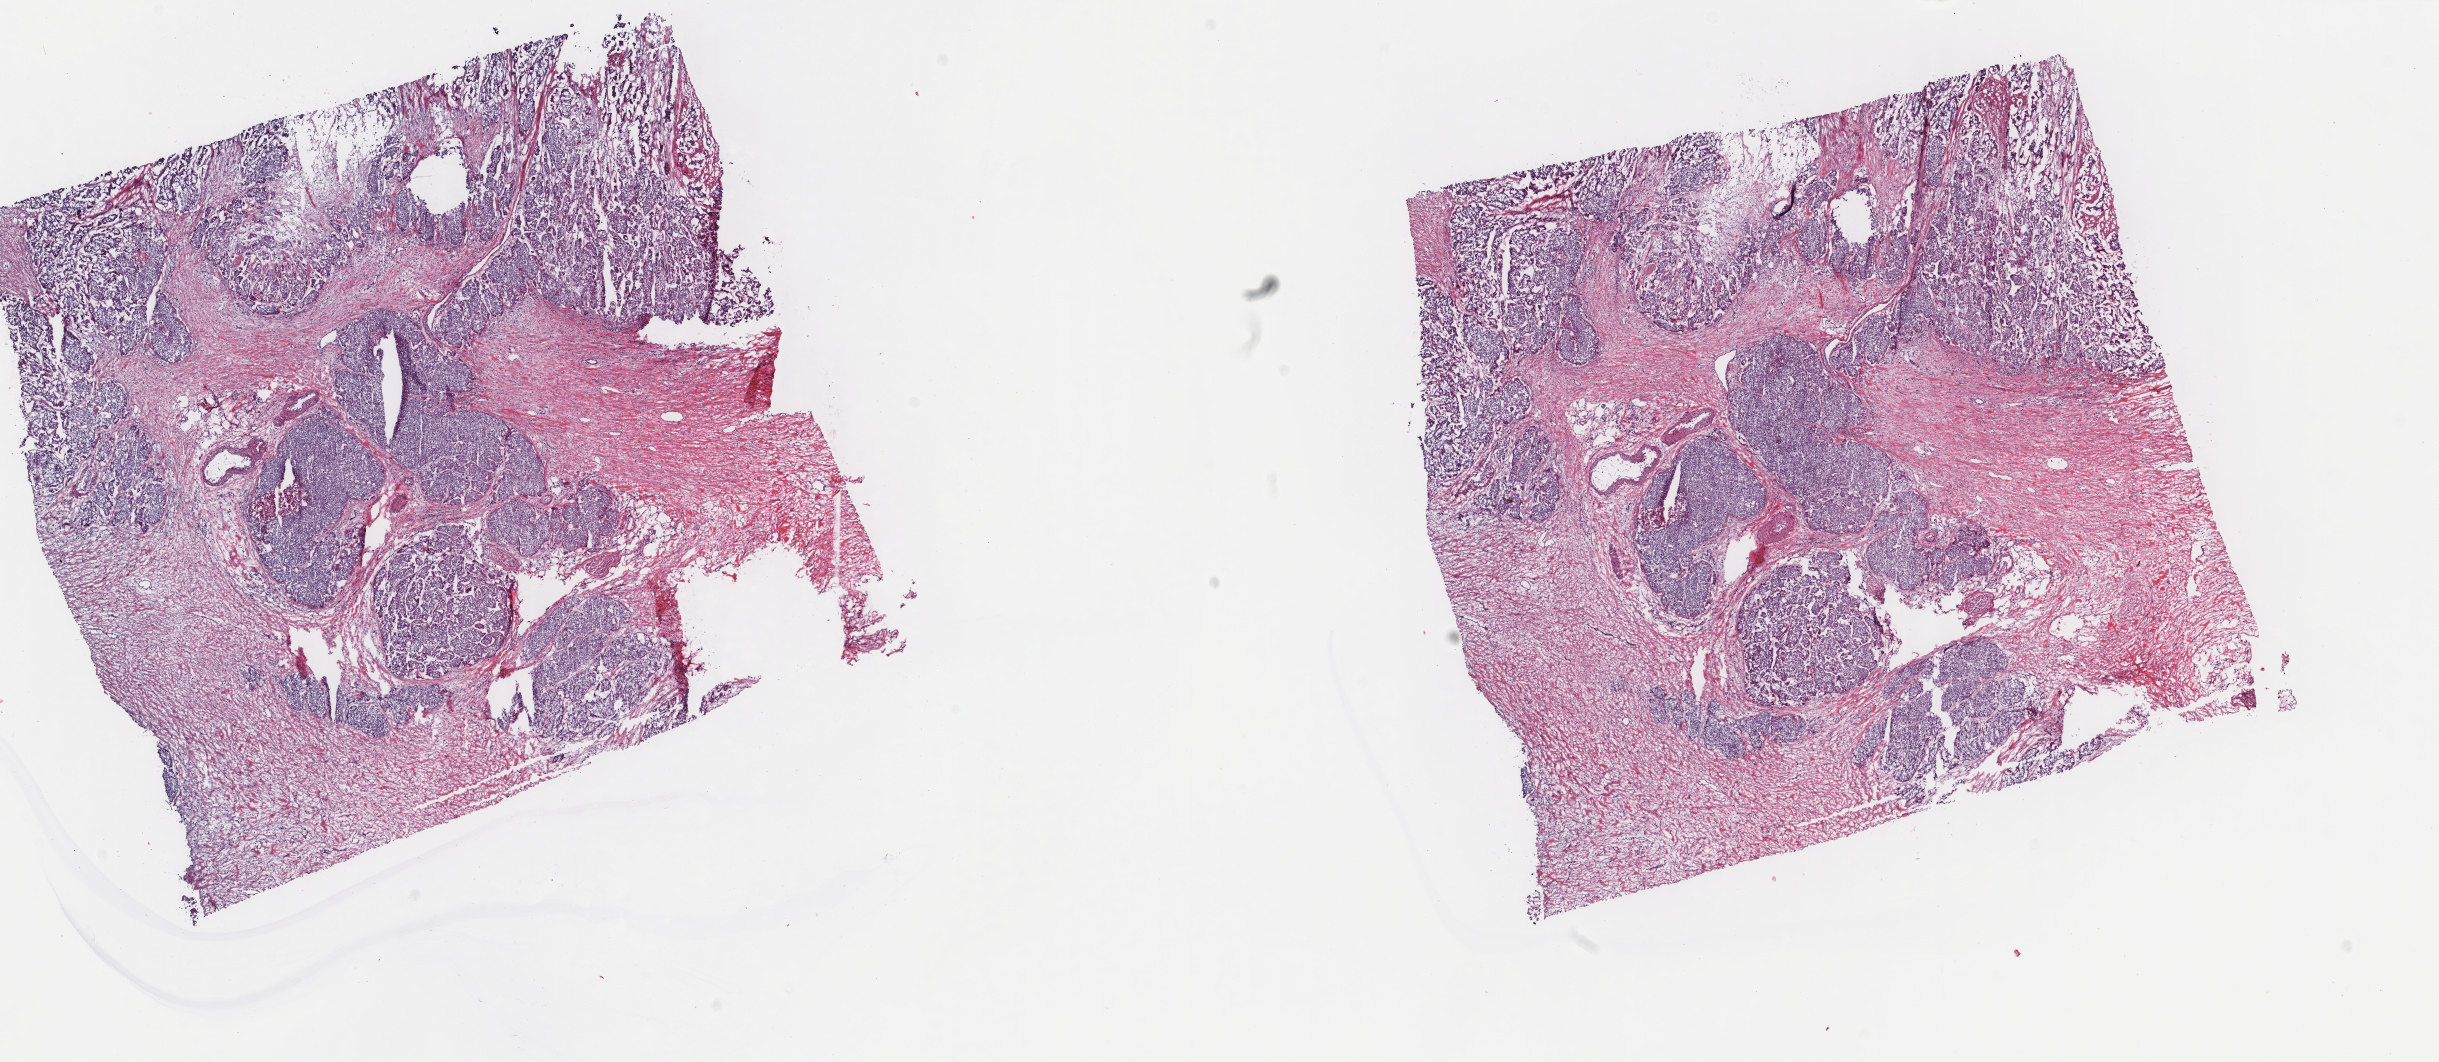
Whole-slide histology image, H&E, shown as a low-resolution overview of the whole scanned area (about 19.4 x 8.4 mm, from a 40x scan); frozen section from the top of the tissue portion; primary tumour sample from the bladder. Male, age 70 years at initial diagnosis. Histologic grade: high grade. Slide review estimates, as recorded: tumour cells 75%, tumour nuclei 75%, normal cells 0%, stromal cells 25%, necrosis 0%. Inflammatory infiltration, as recorded: lymphocyte infiltration 5%, monocyte infiltration 0%, neutrophil infiltration 0%.
AJCC pathologic stage: IV (7th edition). Diagnosis: Transitional cell carcinoma (lateral wall of bladder).